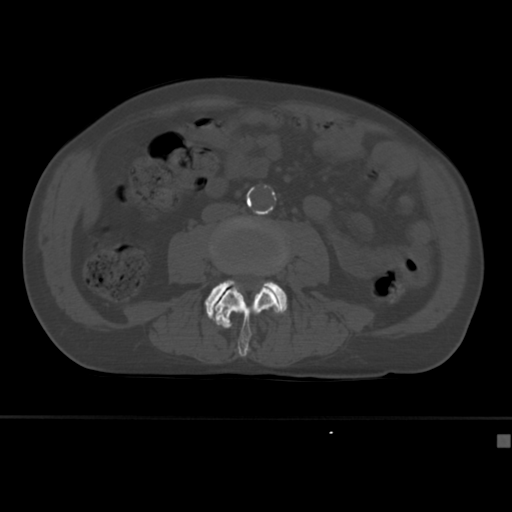
CT including the spine, one axial slice; slice 118 of 430 in the series (ordered by position); reconstruction kernel Br40s; 120 kVp; bone window (W 1800 / L 400 HU); 1.5 mm slice thickness; 512 × 512 image matrix. Male patient, age 64 years. Case-level facts recorded for this patient, not image findings: primary cancer: uterus; vertebrae with lytic lesions (as recorded): T1, T4, T5, T7, L5.
Annotated regions visible in this slice (semi-automatic segmentation, software-assisted and operator-edited):
- L3 vertebra: bounding box <209,217,289,357> (left, top, right, bottom; pixels)
- L4 vertebra: <205,280,288,329>